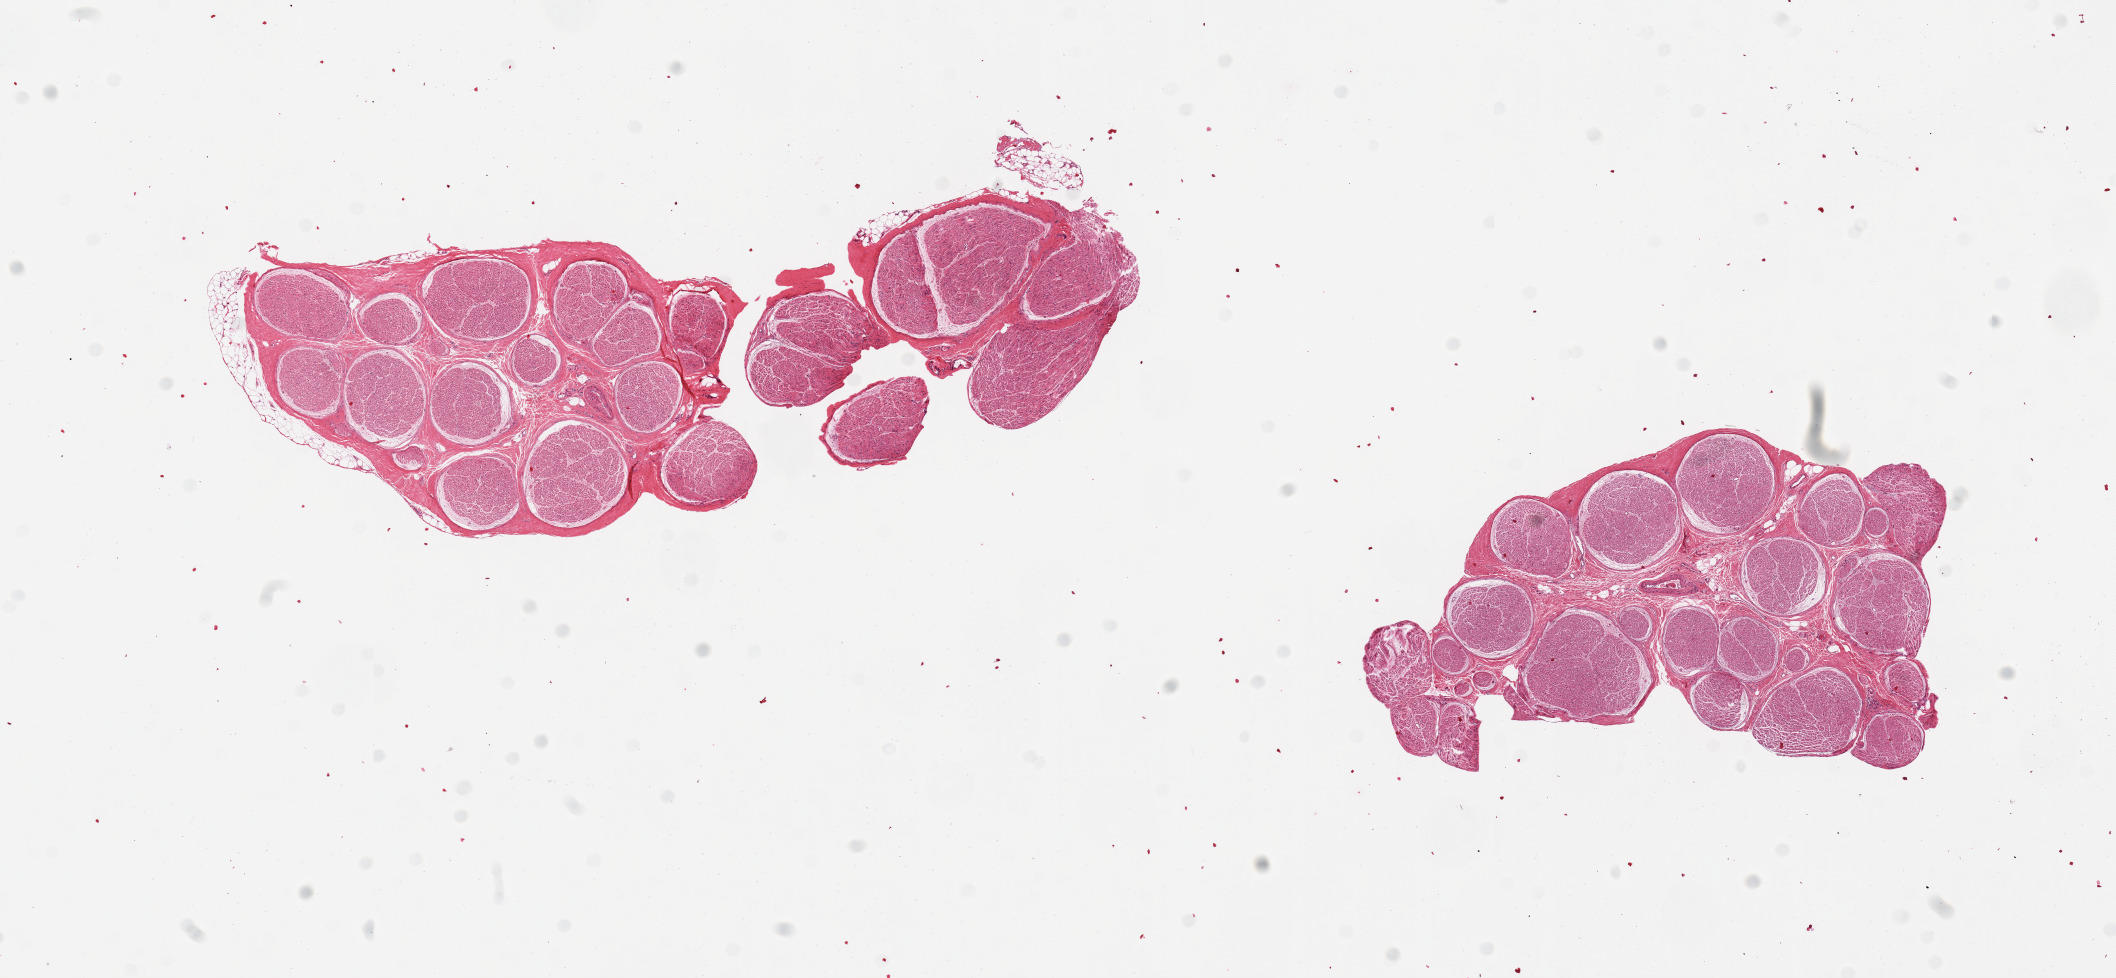
Whole-slide image, hematoxylin and eosin (H&E) stain, brightfield — whole scanned area (about 16.7 x 7.7 mm) shown as a low-resolution overview; PAXgene-fixed paraffin-embedded (PFPE) section; sampled site (target tissue): tibial nerve; tissue donor sample. Donor: male.
* review note (as recorded): 2 pieces, well trimmed